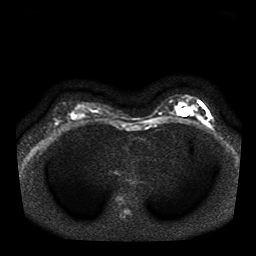
Breast MRI, one axial slice. Slice 21 of 41 in the series (ordered by position). Diffusion-weighted series; image 2 of 4 stored at this slice position (different b-values; order by instance number). 1.5 T. 5 mm slice thickness. 256 × 256 image matrix, field of view 330 × 330 mm. Female patient.
Structures marked on this image (manually delineated by an expert):
- tumour on diffusion-weighted imaging: box from (x=191, y=107) to (x=197, y=113) px